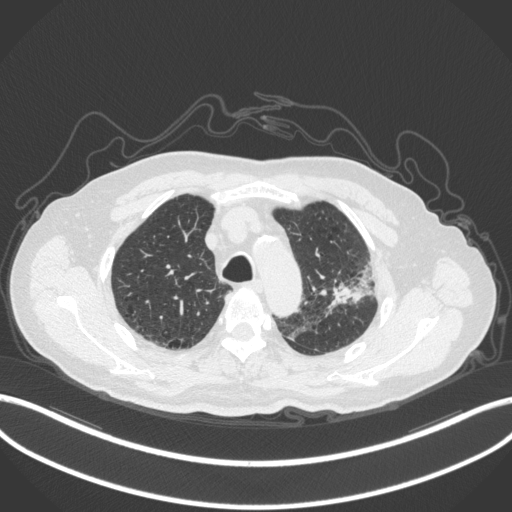
Chest CT, one axial slice; slice 233 of 331 in the series (ordered by position); lung window (W 1500 / L -600 HU); 1 mm slice thickness; 512 × 512 image matrix. Male patient, age 79 years. From the clinical record (not read from this slice): clinical TNM (as recorded): T2a N1 M1.
Outlined on this slice (bounding box drawn by a radiologist):
- lung tumour (recorded histology: adenocarcinoma): bounding box [x1, y1, x2, y2] px = [319, 264, 376, 314]